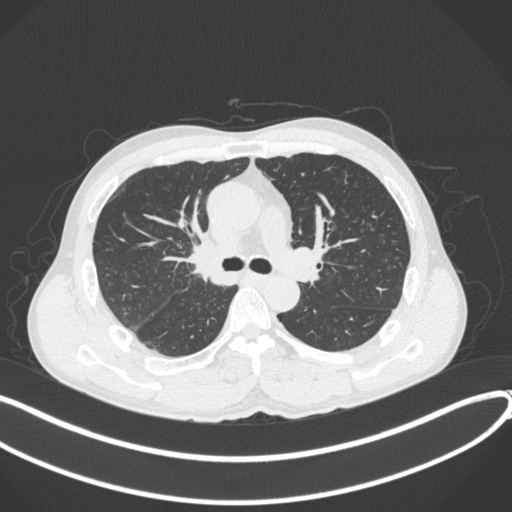
Chest CT, one axial slice; position 243 of 409 along the scan axis; reconstruction kernel B31f; 120 kVp; lung window (W 1500 / L -600 HU); 1 mm slice thickness; 512 × 512 image matrix, field of view 400 × 400 mm. Male patient, age 53 years. From the clinical record (not read from this slice): clinical TNM (as recorded): T1b N0 M0.
Structures marked on this image (bounding box drawn by a radiologist):
- lung tumour (recorded histology: squamous cell carcinoma): bounding box (x1, y1, x2, y2) in pixels: (186, 233, 240, 289)